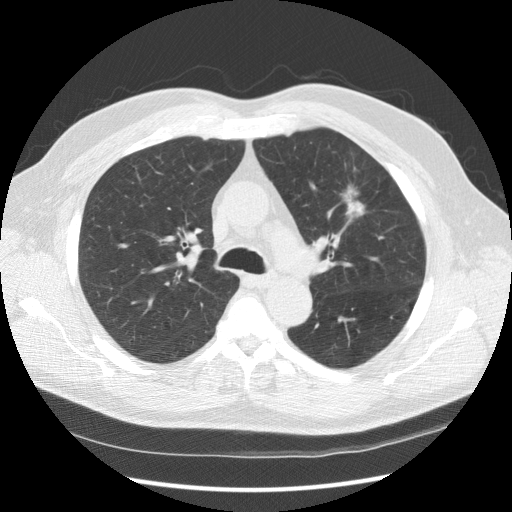
Low-dose screening chest CT, one axial slice. Position 104 of 157 along the scan axis. Reconstruction kernel STANDARD. 120 kVp. Lung window (W 1500 / L -600 HU). 512 × 512 image matrix, field of view 370 × 370 mm.
Outlined on this slice (outlined manually by an expert reader):
- lesion 1 (tumor, upper lobe of left lung): bounding box [x1, y1, x2, y2] px = [342, 186, 365, 219]